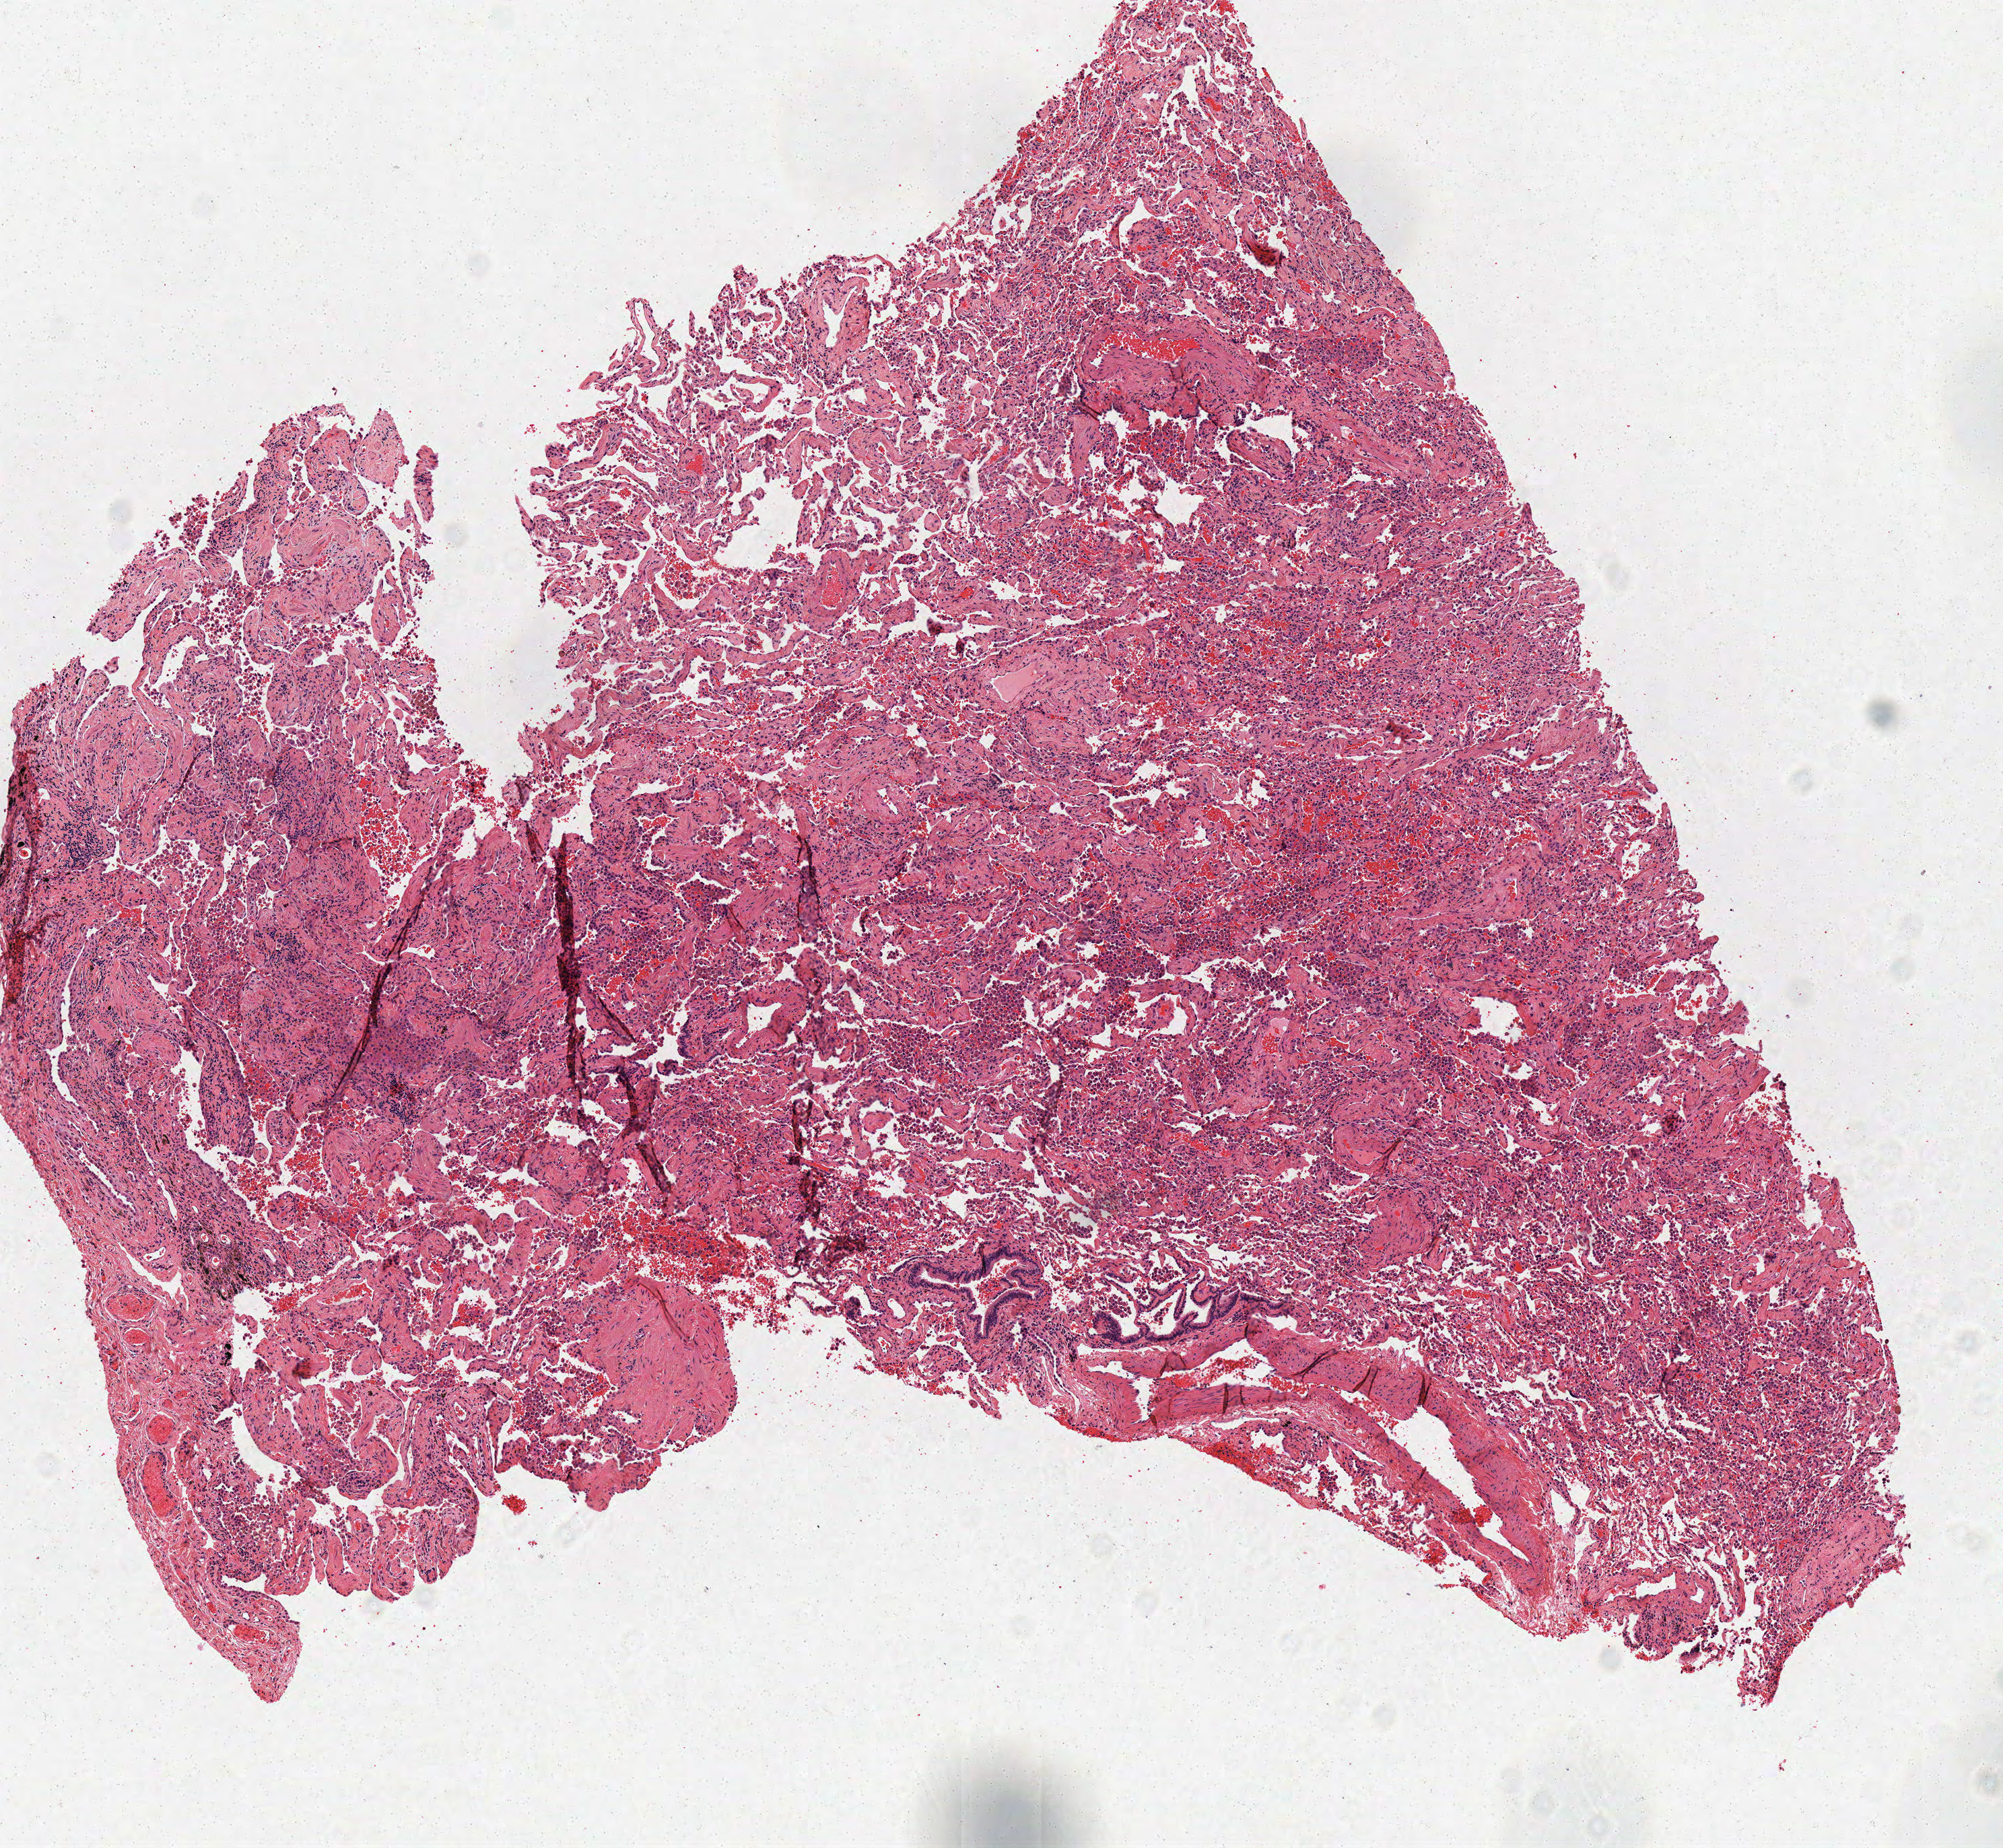
Hematoxylin and eosin (H&E) stained whole-slide image — a low-resolution overview of the entire scanned area, about 5.9 x 5.4 mm (from a 40x scan), frozen section, solid tissue normal (non-tumour tissue) sample from the lung. Male, age 78 years at initial diagnosis.
This section: solid tissue normal (non-tumour) sample from the same patient. Patient diagnosis: Bronchiolo-alveolar carcinoma, non-mucinous.